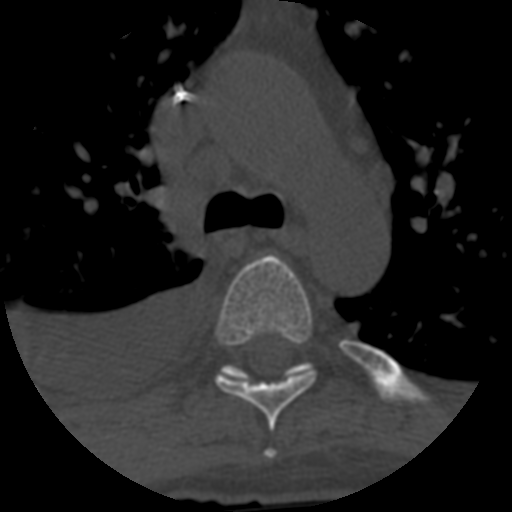
CT including the spine, one axial slice; slice 450 of 708 in the series (ordered by position); reconstruction kernel STANDARD; one of 3 acquisitions stored at this slice position; bone window (W 1800 / L 400 HU); 1.25 mm slice thickness; 512 × 512 image matrix, field of view 160 × 160 mm. Patient age 55 years. Case-level facts recorded for this patient, not image findings: primary cancer: colon; vertebrae with lytic lesions (as recorded): T12, L1, L5.
Outlined on this slice (semi-automatic segmentation, software-assisted and operator-edited):
- T4 vertebra: bounding box <265,450,275,458> (left, top, right, bottom; pixels)
- T5 vertebra: <215,255,316,431>
- T6 vertebra: <220,362,314,380>